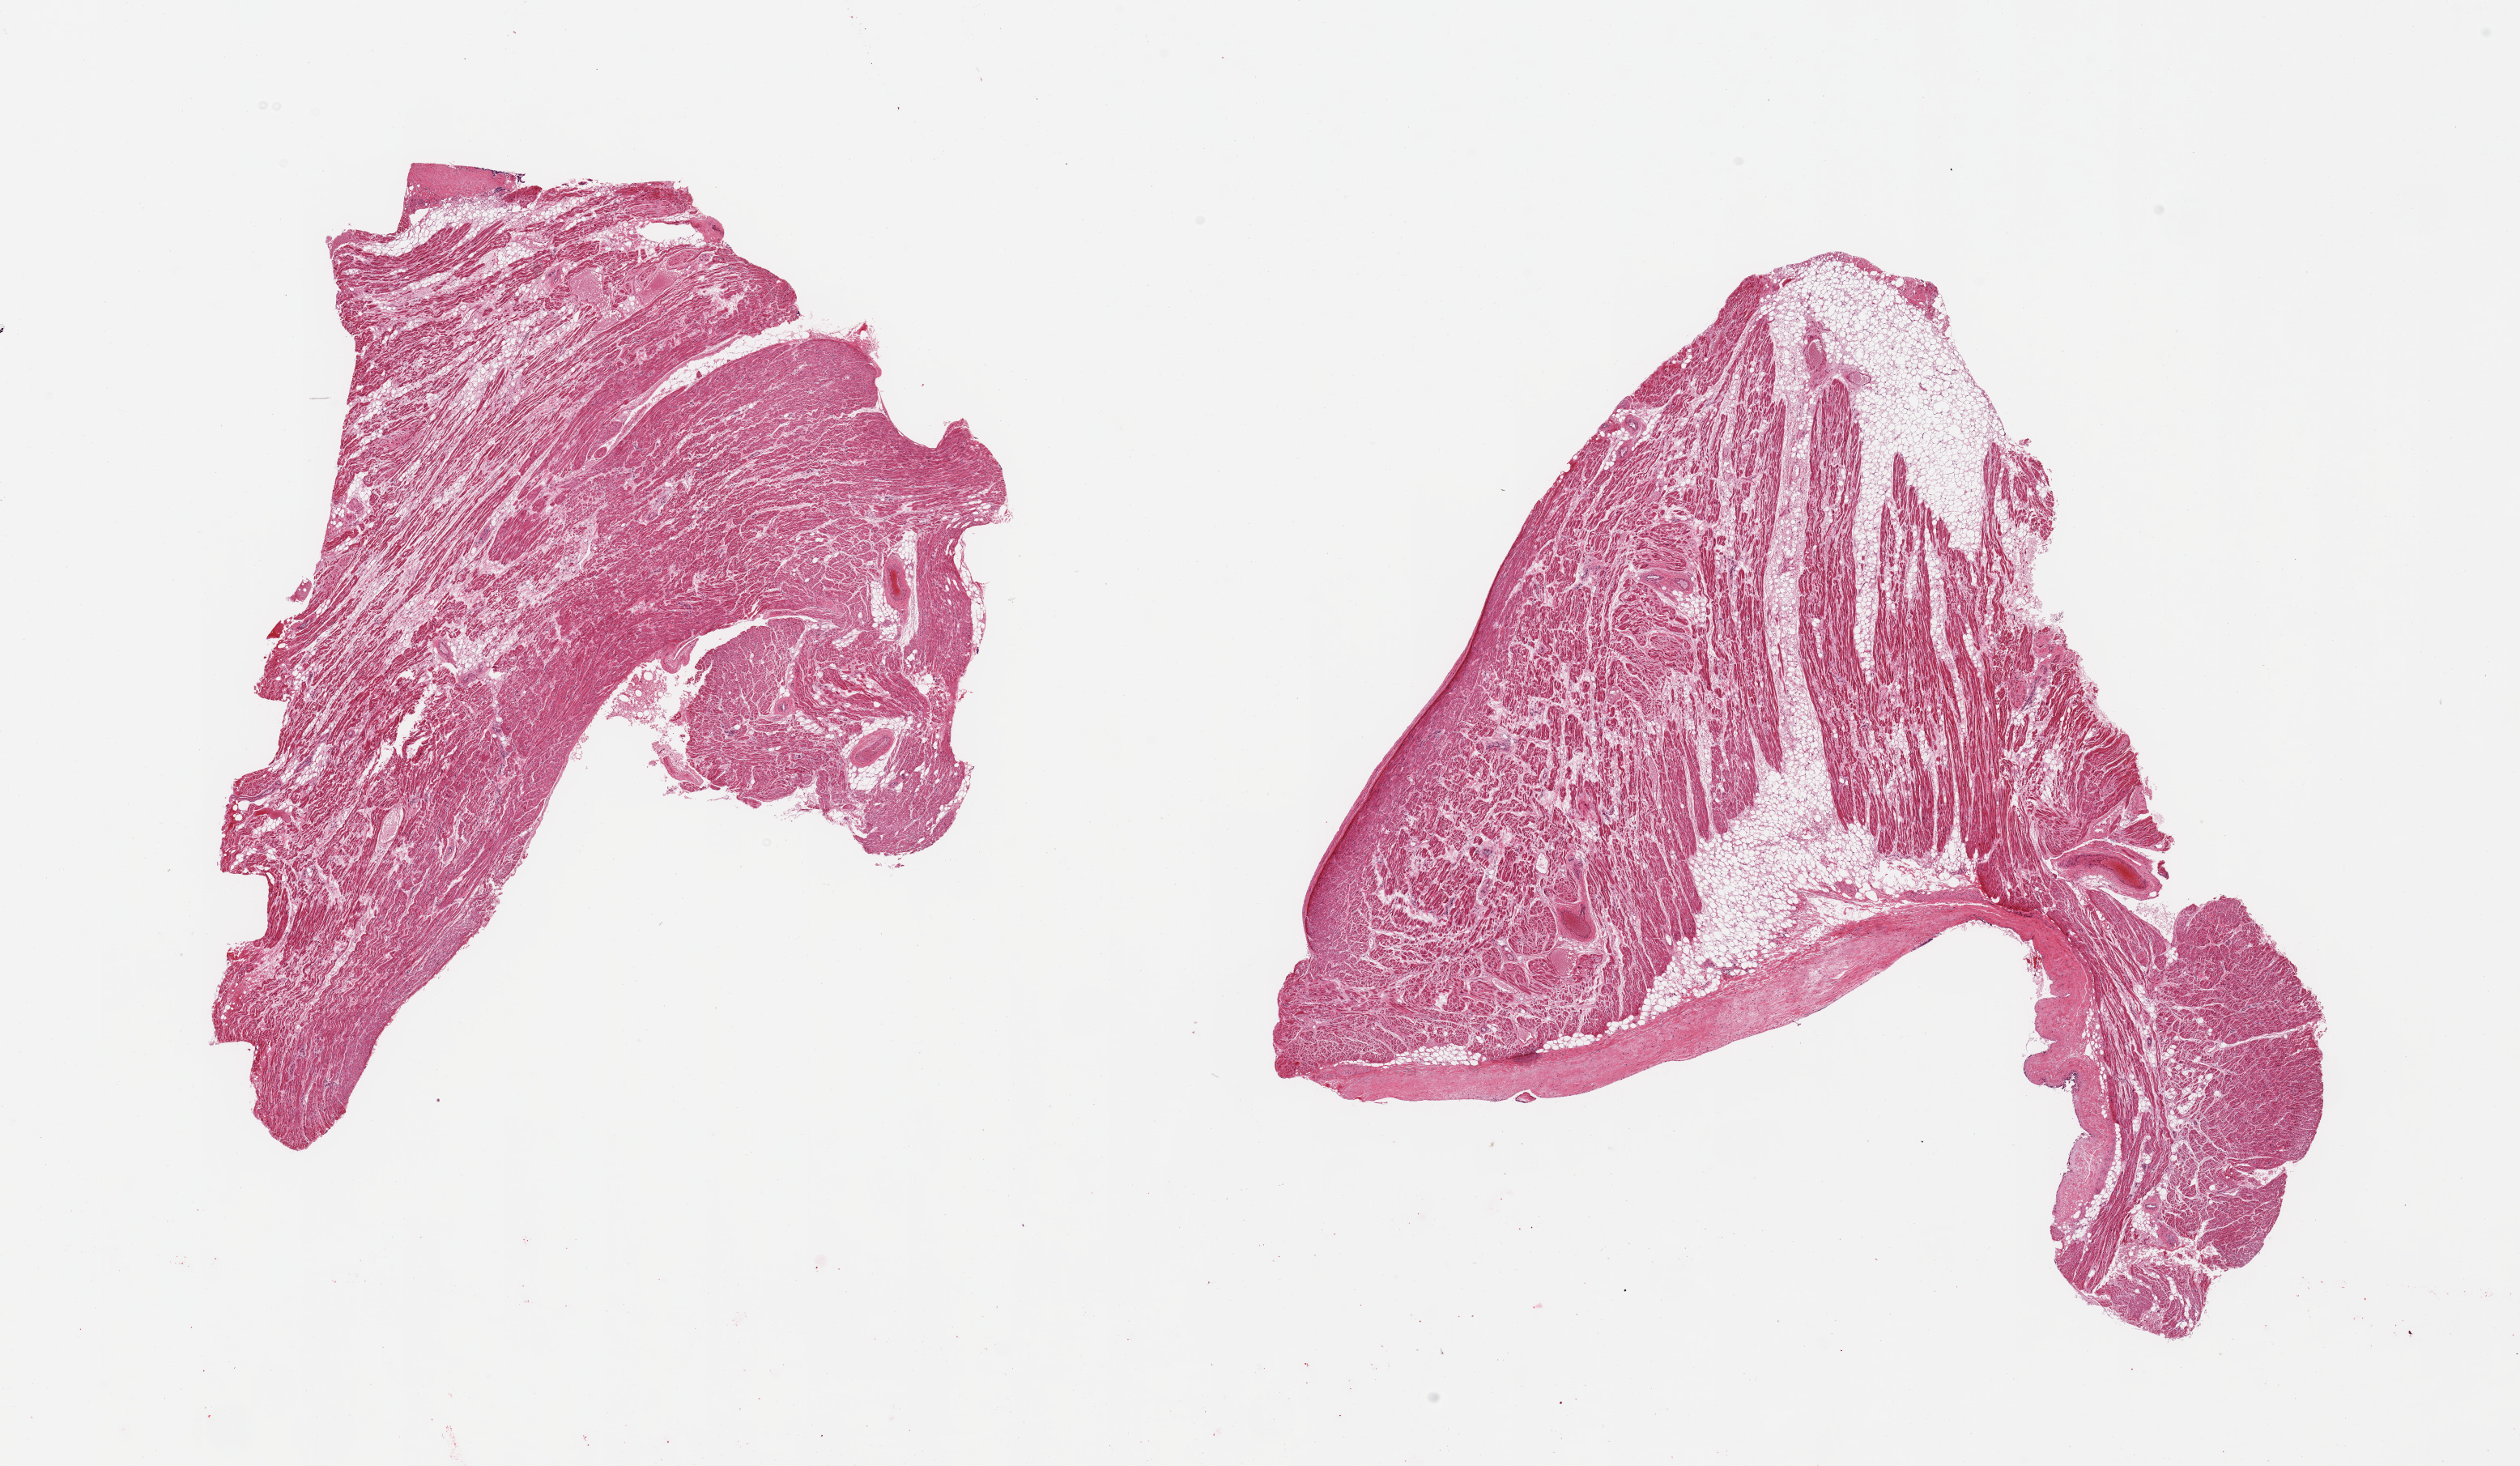
H&E whole-slide image, whole scanned area (about 24.6 x 14.3 mm) shown as a low-resolution overview. PAXgene-fixed paraffin-embedded (PFPE) section. Section of auricular appendage (target tissue). Tissue donor sample. Female donor.
Reviewer comment on this tissue sample: 2 pieces, no abnormalities.